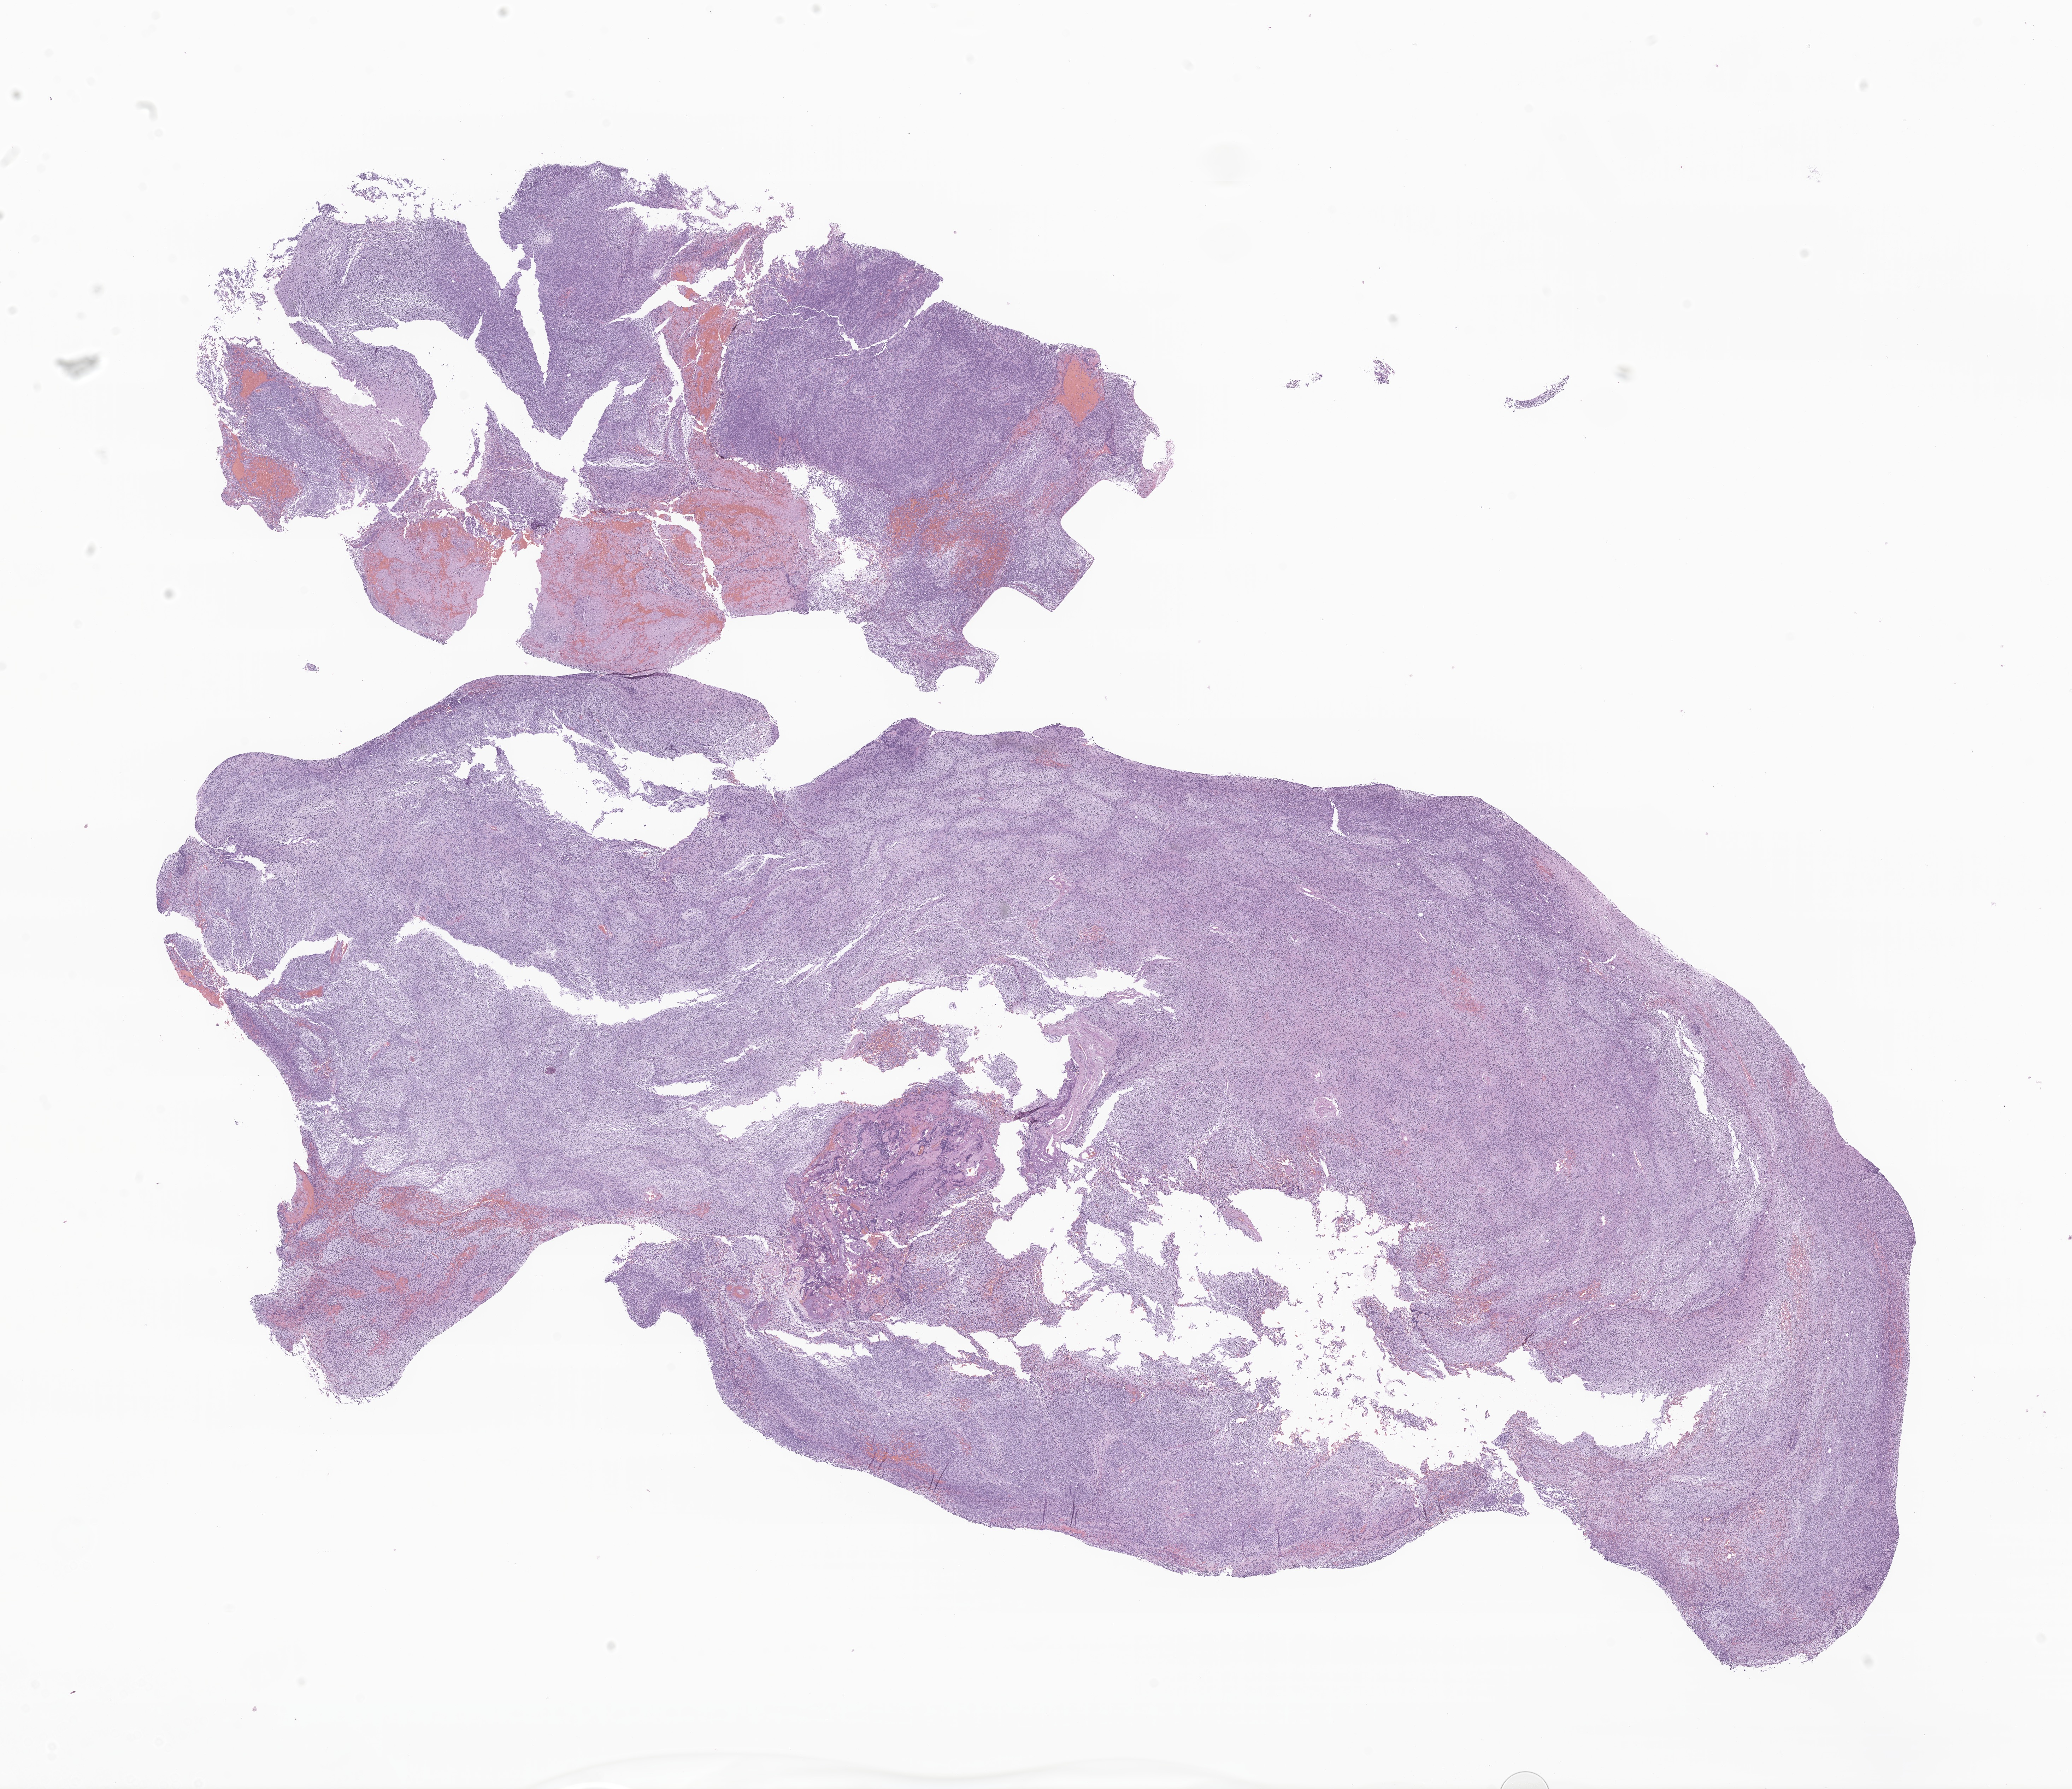
Whole-slide image, H&E stain of tumor tissue from the brain — low-resolution overview of the scanned area, about 24.7 x 21.3 mm. FFPE section. Patient: male, age 107 months (8 years 11 months).
Diagnosis: Medulloblastoma, NOS.